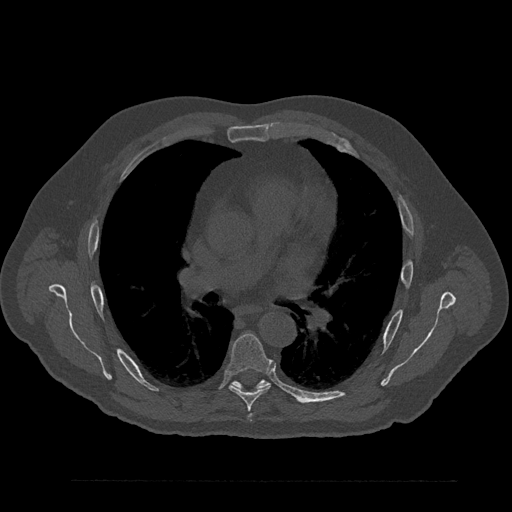
CT including the spine, one axial slice; slice 542 of 797 in the series (ordered by position); reconstruction kernel Br40s/3; 120 kVp; bone window (W 1800 / L 400 HU); 512 × 512 image matrix, field of view 430 × 430 mm. Patient: male, 61 years. From the clinical record (not read from this slice): primary cancer: prostate.
Annotated regions visible in this slice (semi-automatic segmentation, software-assisted and operator-edited):
- T6 vertebra: bounding box [x1, y1, x2, y2] px = [227, 334, 273, 422]
- T7 vertebra: [233, 380, 269, 389]